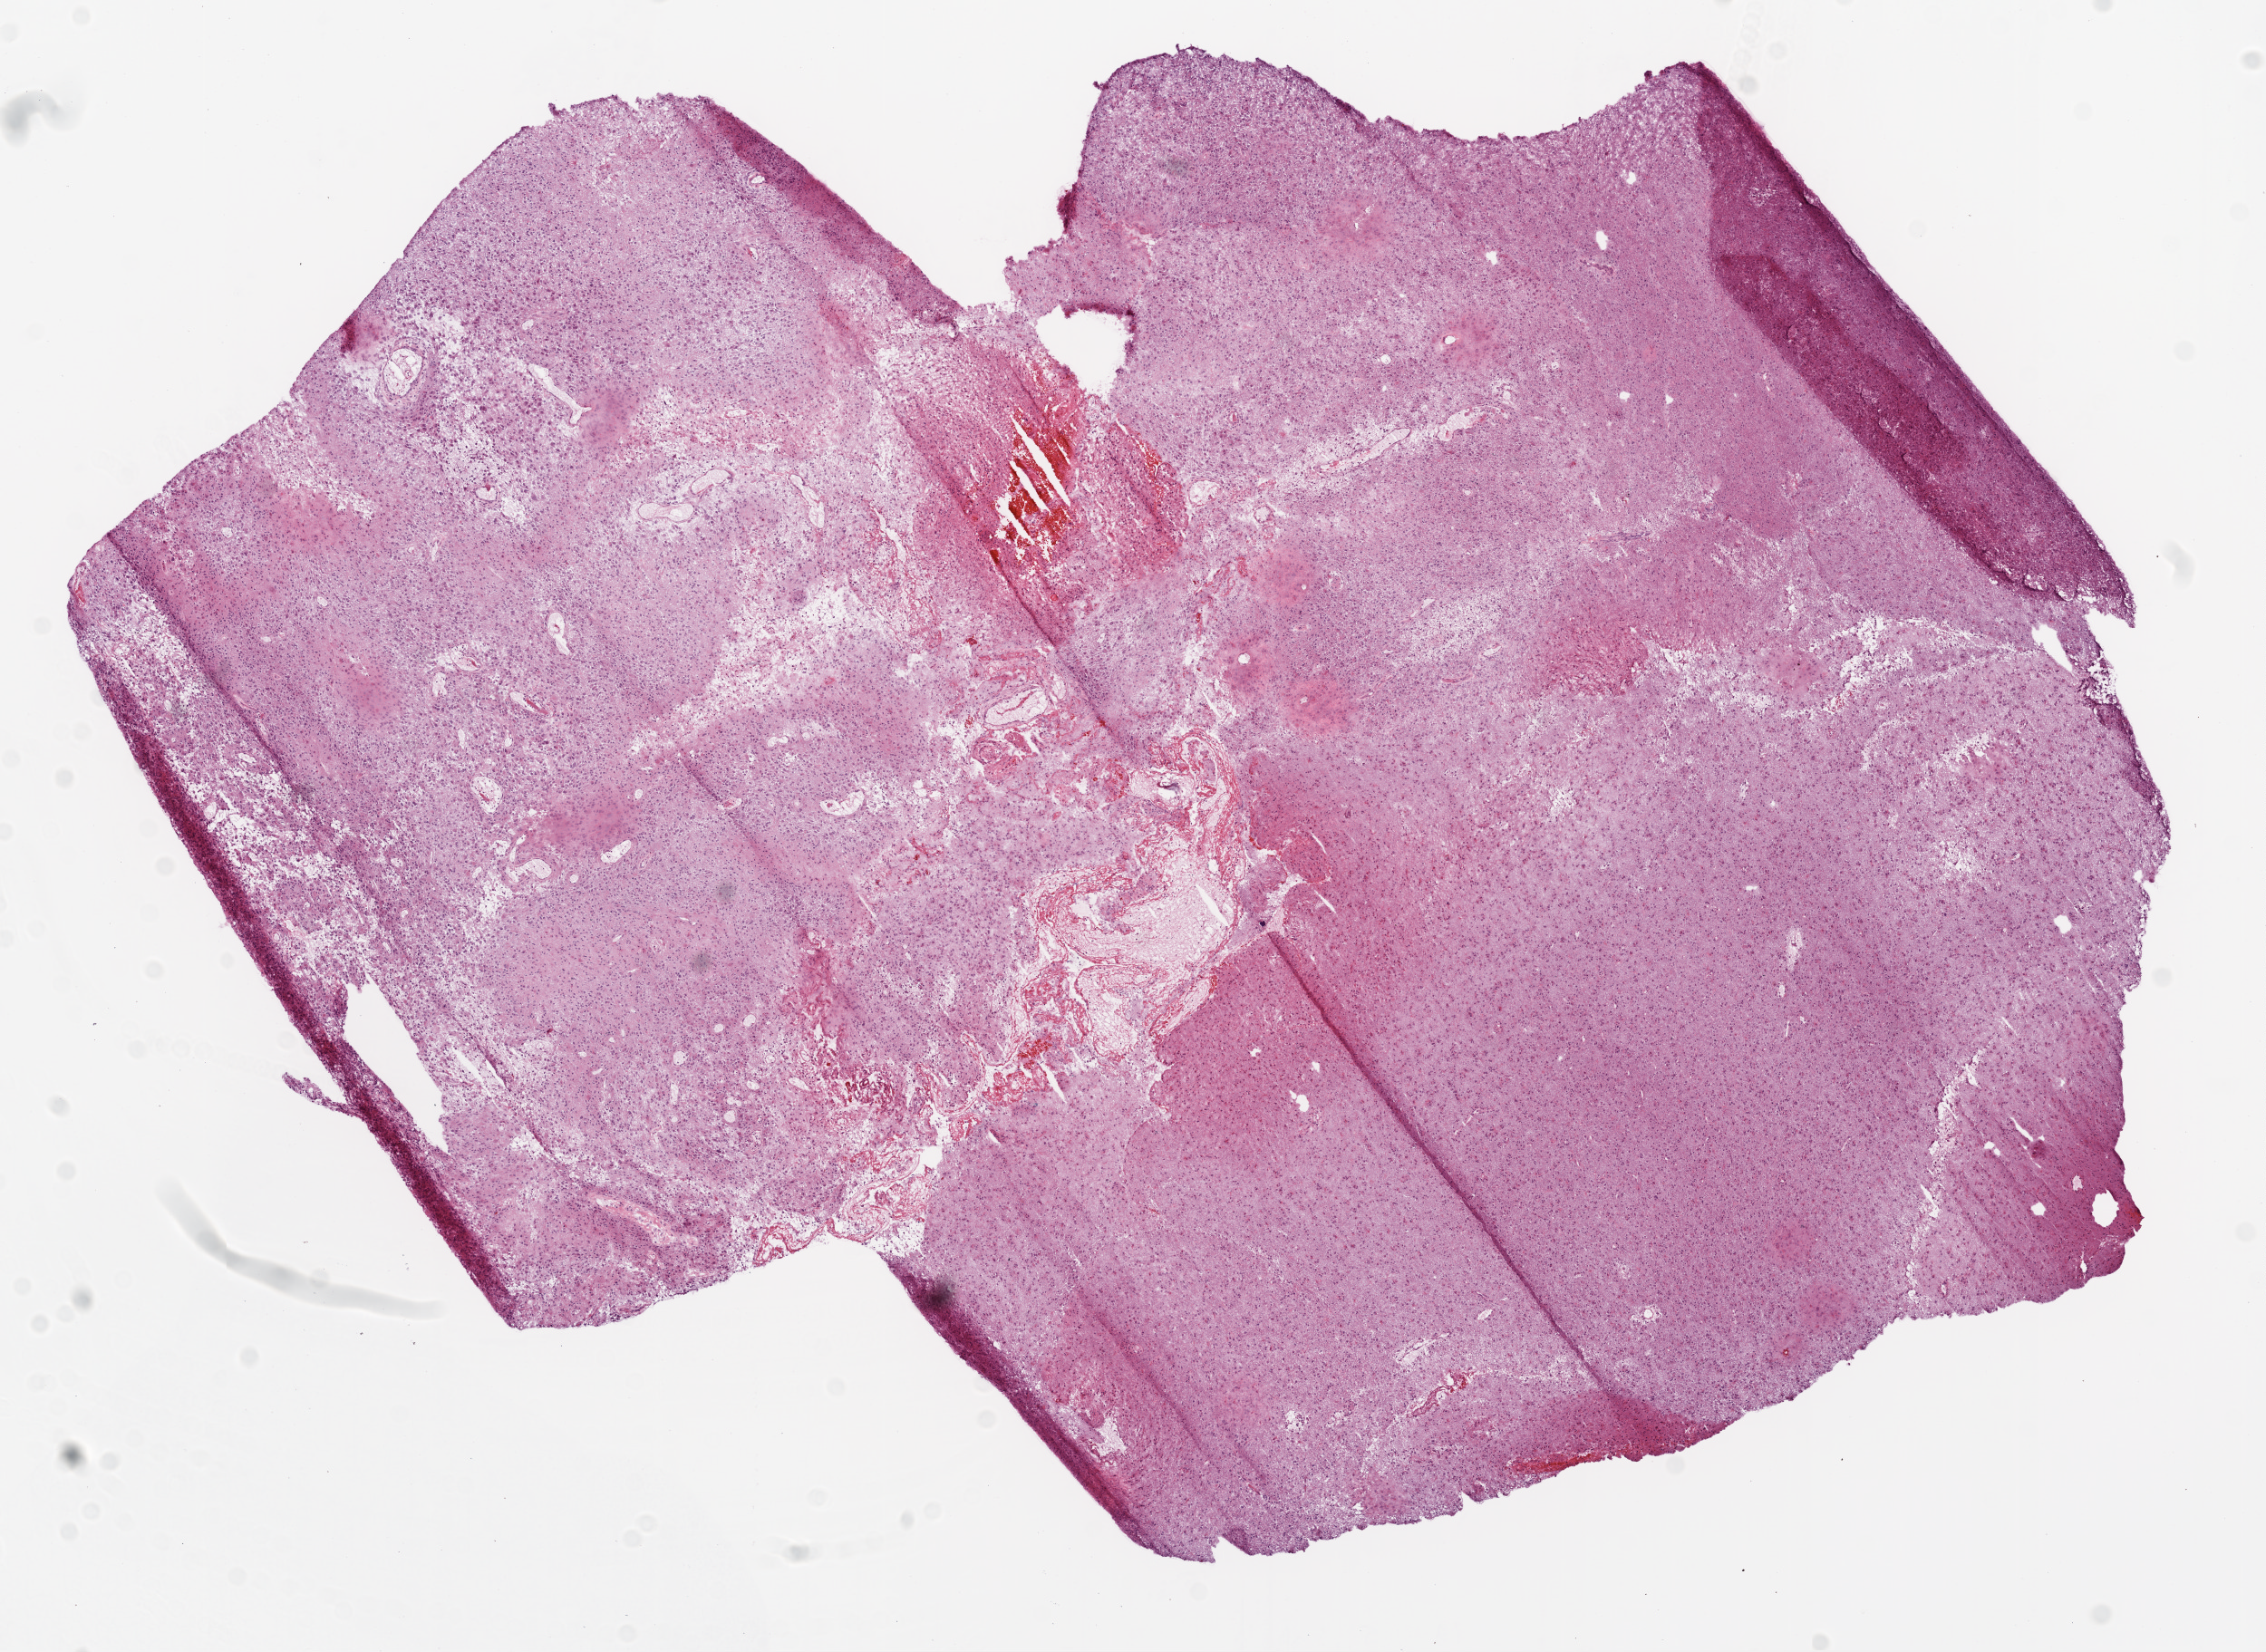
Hematoxylin and eosin (H&E) stained whole-slide image, shown as a low-resolution overview of the whole scanned area (about 10.0 x 7.3 mm), frozen section, primary tumour sample from the brain. Patient: male, age at initial diagnosis 60 years. Slide review estimates, as recorded: tumour cells 100%, tumour nuclei 85%, normal cells 0%, stromal cells 0%, necrosis 0%.
Histologic diagnosis: Glioblastoma.